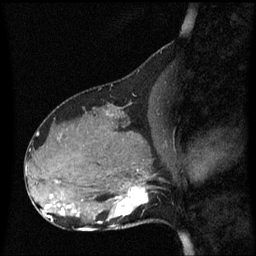
Breast MRI (dynamic contrast-enhanced), one sagittal slice. Position 25 of 60 along the scan axis. Dynamic contrast-enhanced series, image 2 of 3 at this slice position (ordered by acquisition). 1.5 T. TE 4.2 ms, TR 8.4 ms. 2.1 mm slice thickness. 256 × 256 image matrix. Female patient, age 31 years. Case-level facts recorded for this patient, not image findings: setting: breast cancer imaged before/during neoadjuvant chemotherapy; receptor status: HR-positive, HER2-negative.
Annotated regions visible in this slice (semi-automatic segmentation, software-assisted and operator-edited):
- analysis volume of interest (the breast-tissue region the enhancement analysis was run in; not a lesion): bounding box (x1, y1, x2, y2) in pixels: (98, 175, 161, 228)
- tumour enhancement mask (voxels above the 70 % enhancement threshold inside the analysis volume of interest): (99, 187, 149, 224)